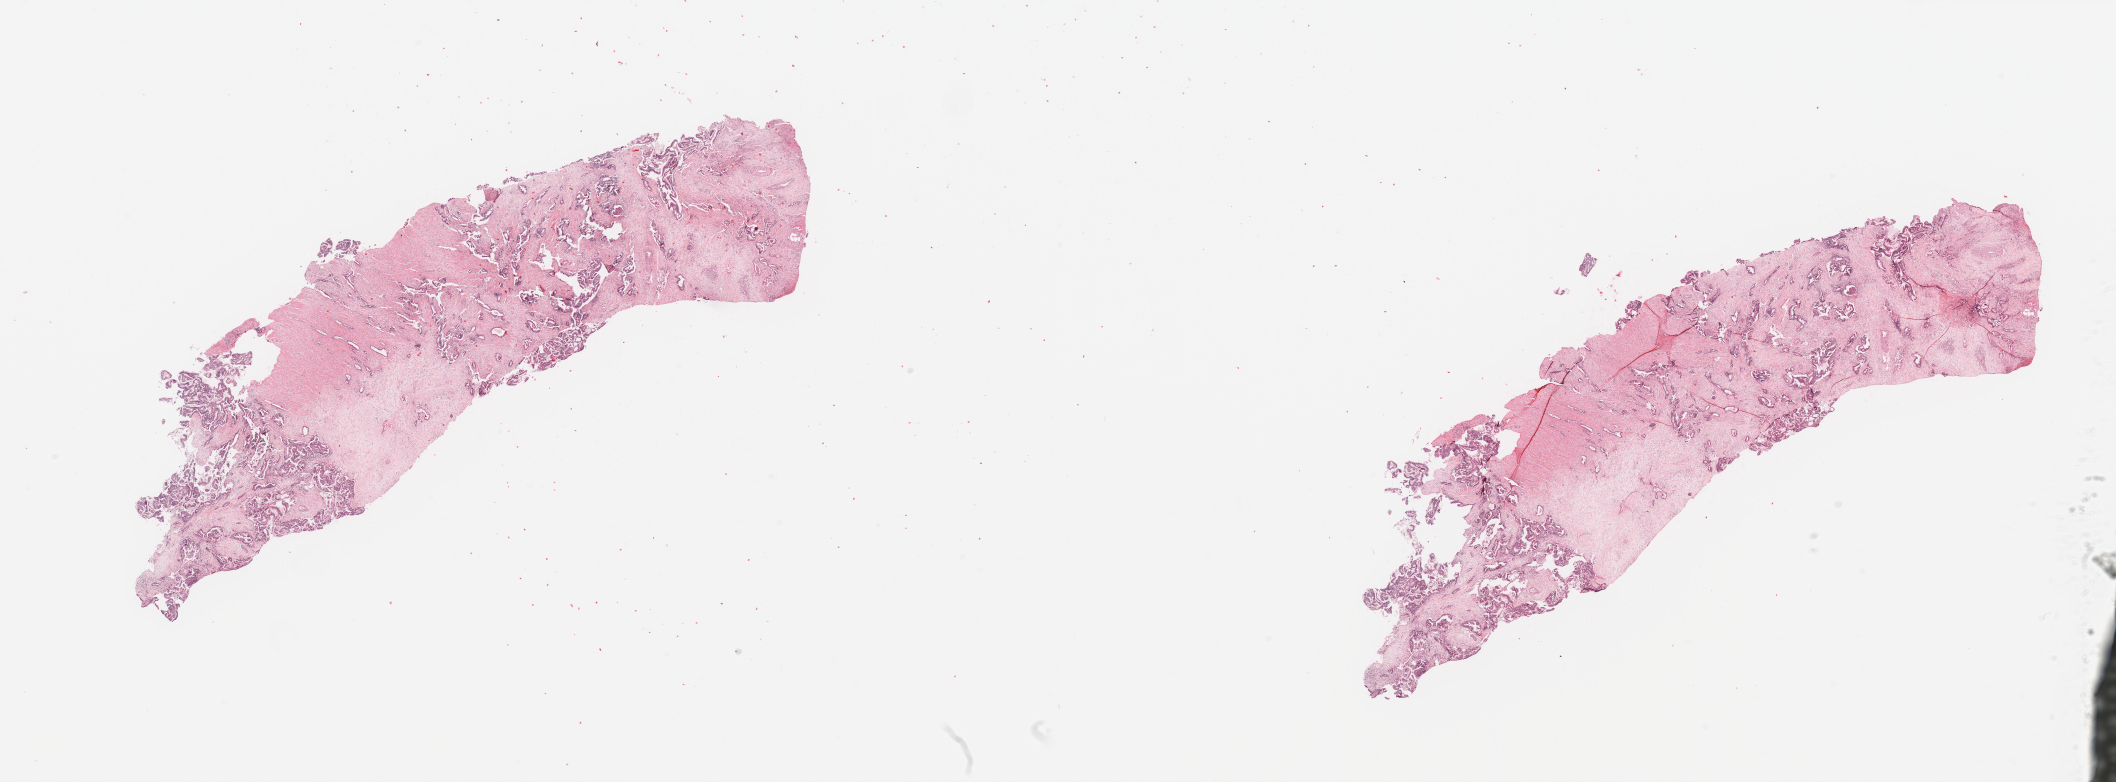
Whole-slide histology image, H&E — a low-resolution overview of the entire scanned area, about 33.5 x 12.4 mm (acquisition: 20x scan). Tumour tissue sample, pancreas. 62-year-old female patient. Histologic grade: G3 (poorly differentiated).
• AJCC pathologic stage: III
• primary tumour site (as recorded): head
• histologic diagnosis: Infiltrating duct carcinoma, NOS